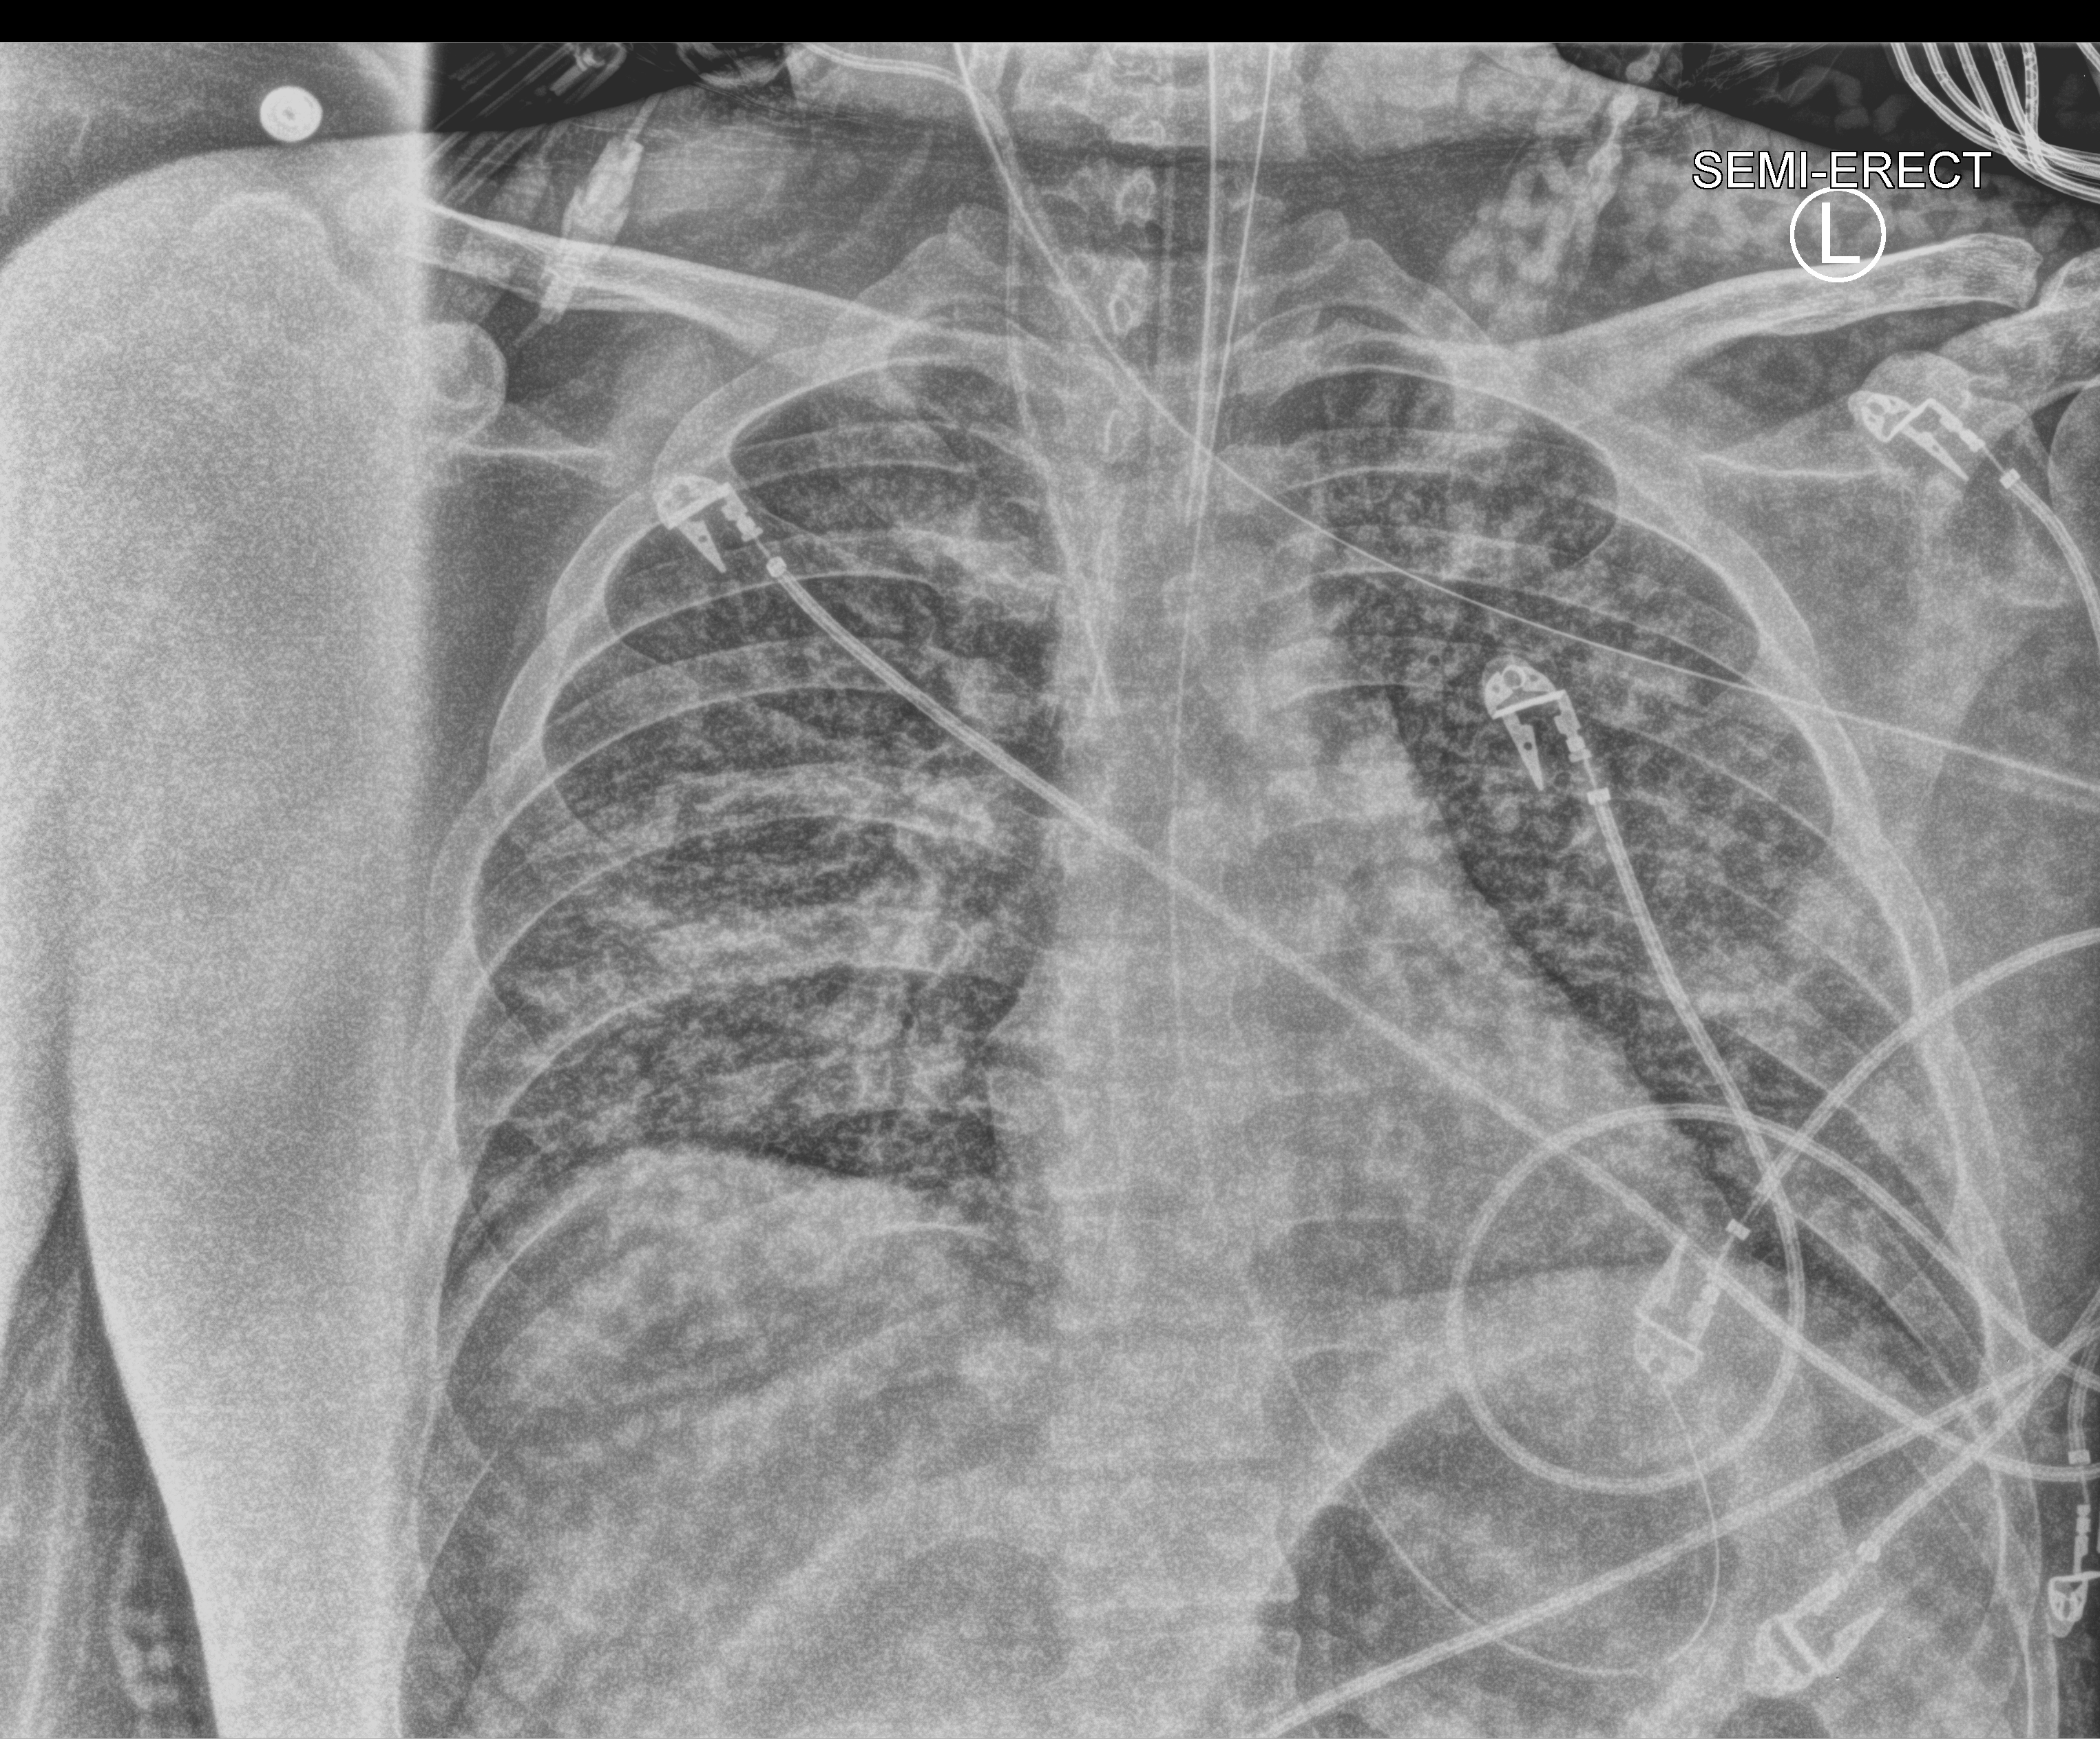
Bedside chest radiograph (computed radiography). Patient hospitalised with COVID-19; male, aged 18–59 years.
Admission-level facts for this patient (not findings on this image; timing relative to this image not recorded): admitted to intensive care during this hospital stay: yes.